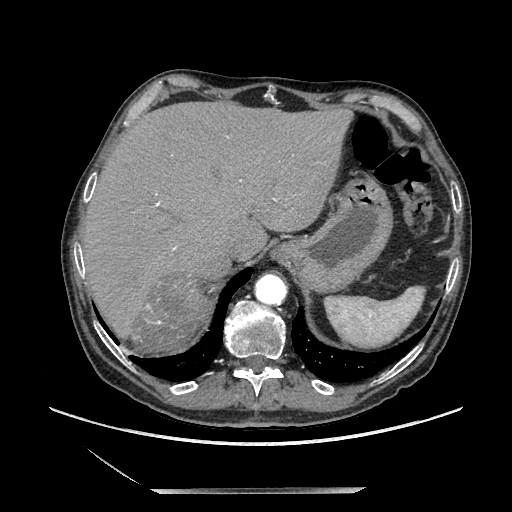
Contrast-enhanced abdominal CT, one axial slice; soft-tissue window (W 400 / L 40 HU); 1.25 mm slice thickness; 512 × 512 image matrix, field of view 420 × 420 mm. Male patient. From the clinical record (not read from this slice): diagnosis: adrenocortical carcinoma; tumour side: right adrenal; tumour size at pathology: 16 cm; Ki-67 index: 17 %; stage (as recorded): 3.
Outlined on this slice (semi-automatically segmented with operator editing):
- mass: bounding box <130,277,210,352> (left, top, right, bottom; pixels)